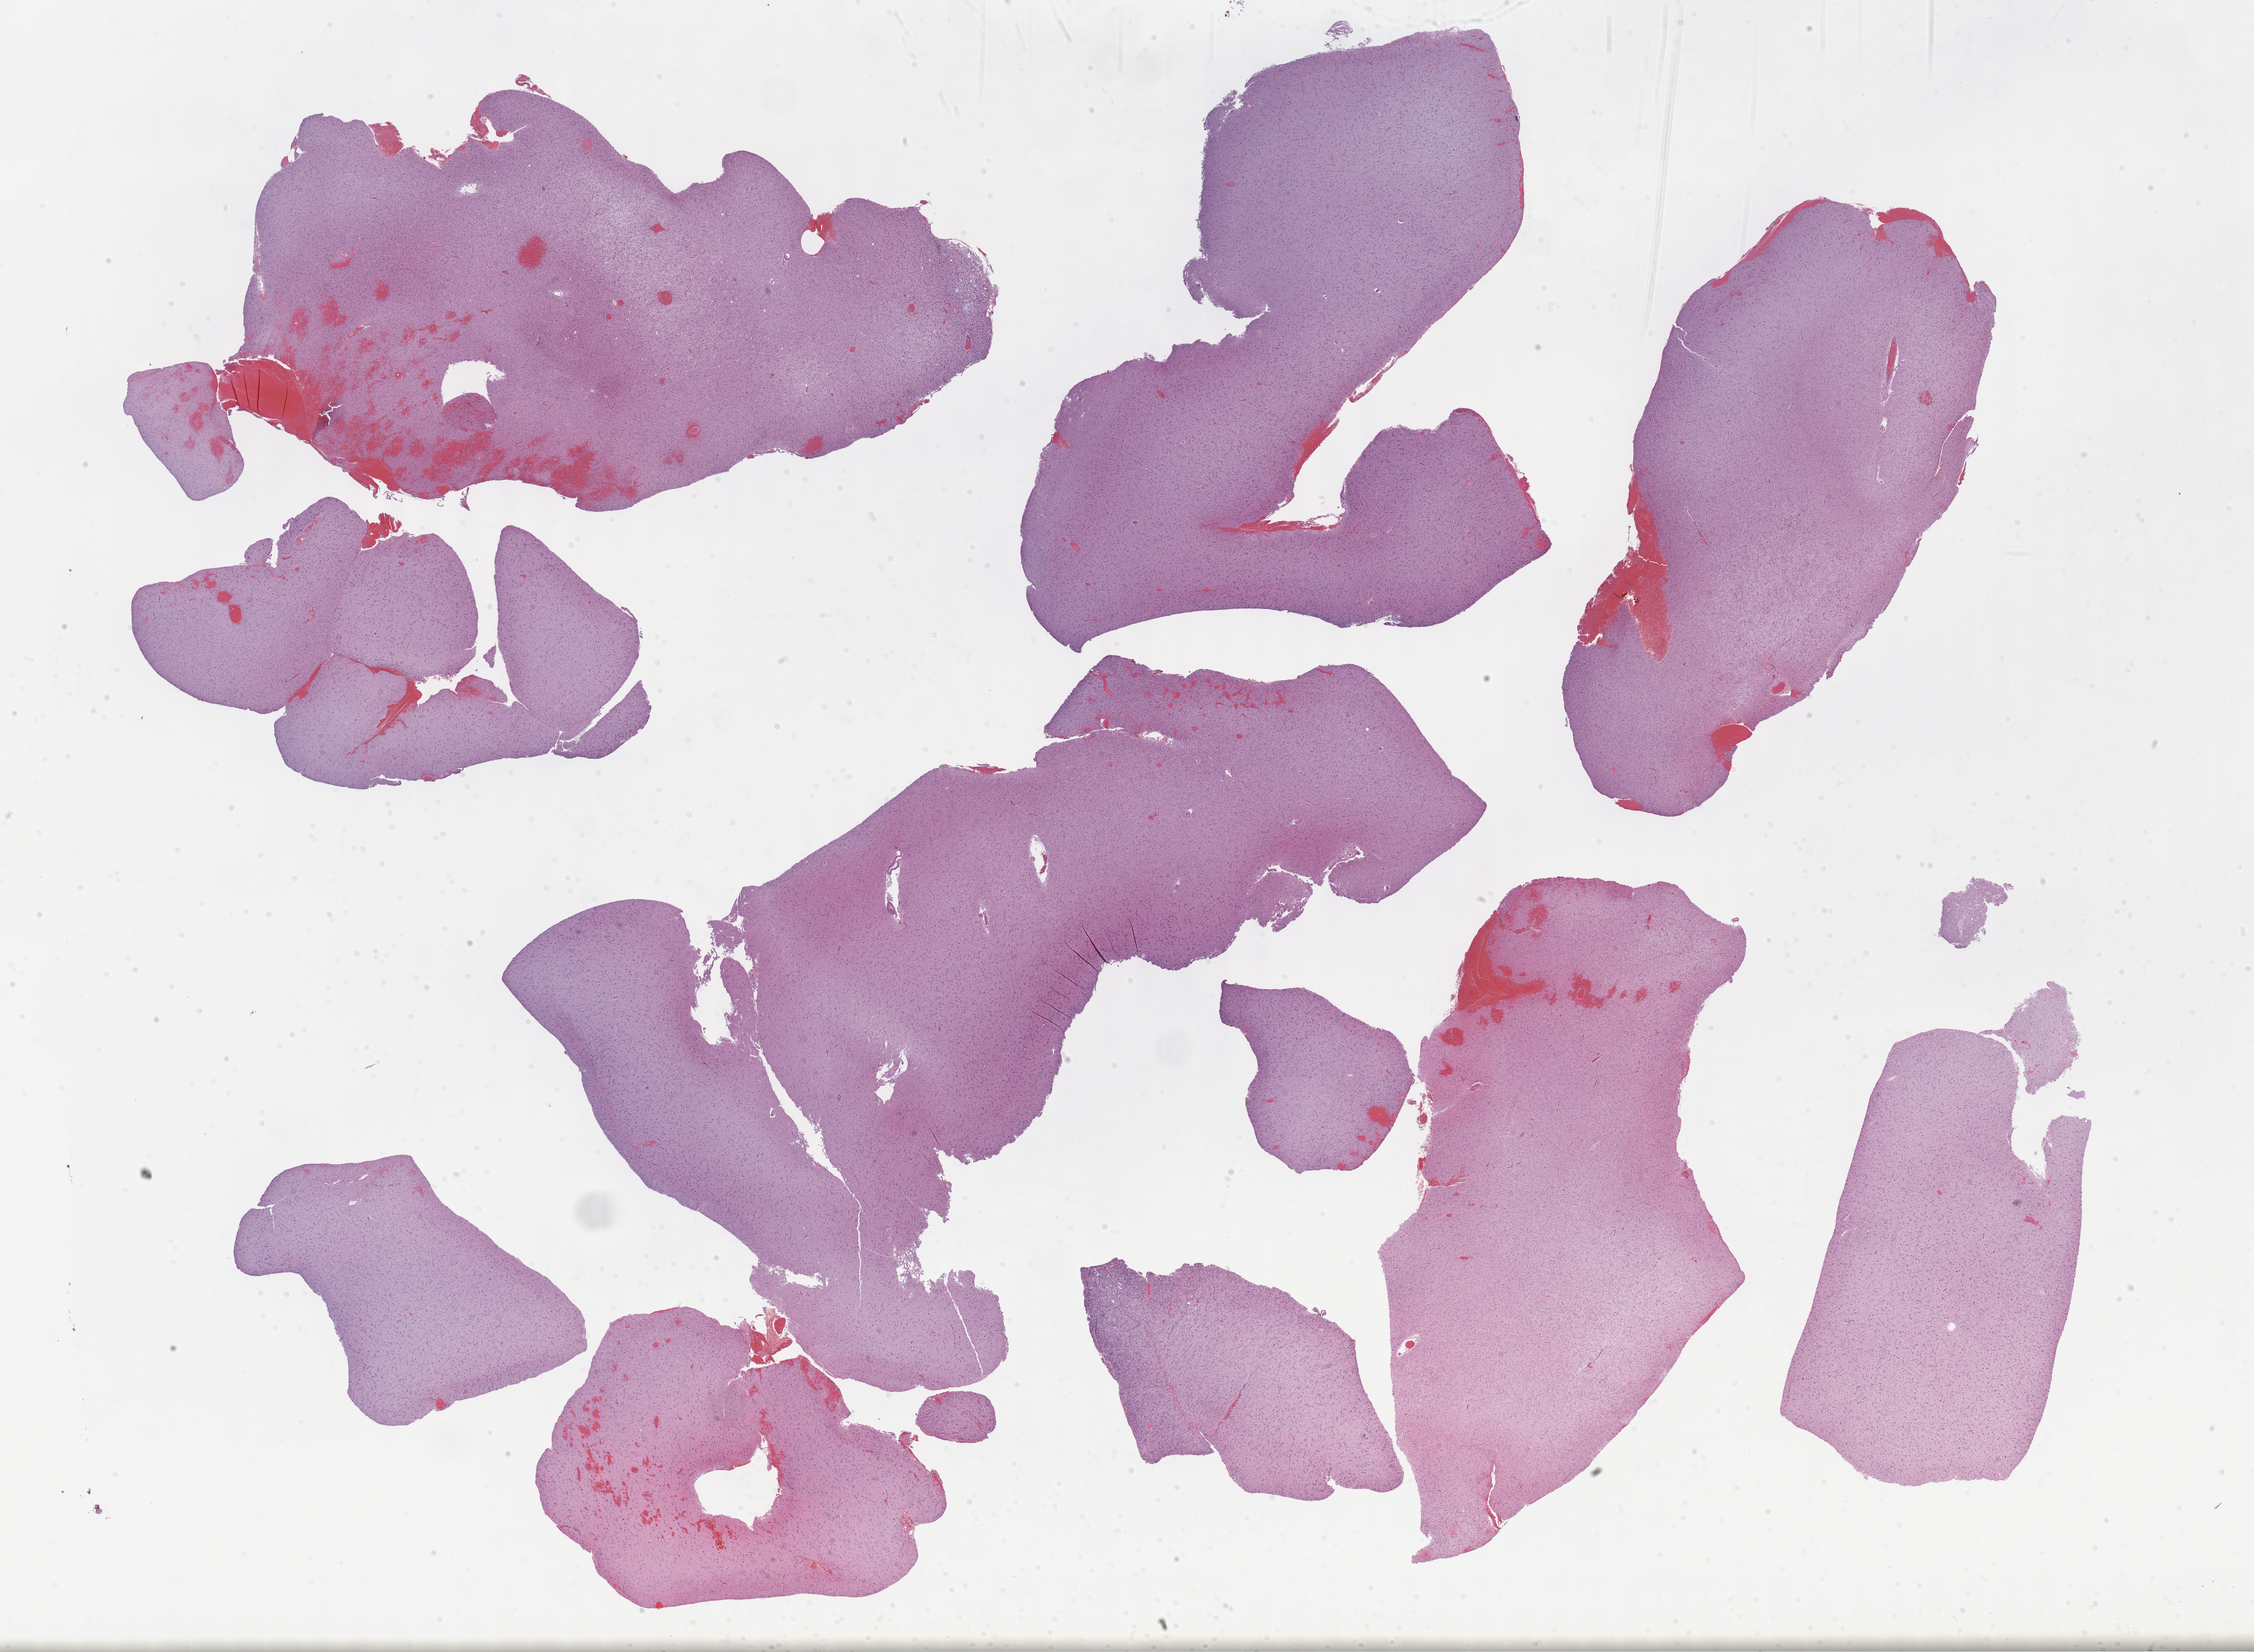
Whole-slide histology image, Hematoxylin and eosin (H&E) stained, whole scanned area (about 30.2 x 22.1 mm, slide scanned at 40x) shown as a low-resolution overview, formalin-fixed paraffin-embedded (FFPE) diagnostic section, brain, primary tumour sample. Male patient; age at initial diagnosis 54 years.
Histologic diagnosis: Oligodendroglioma, NOS (cerebrum).